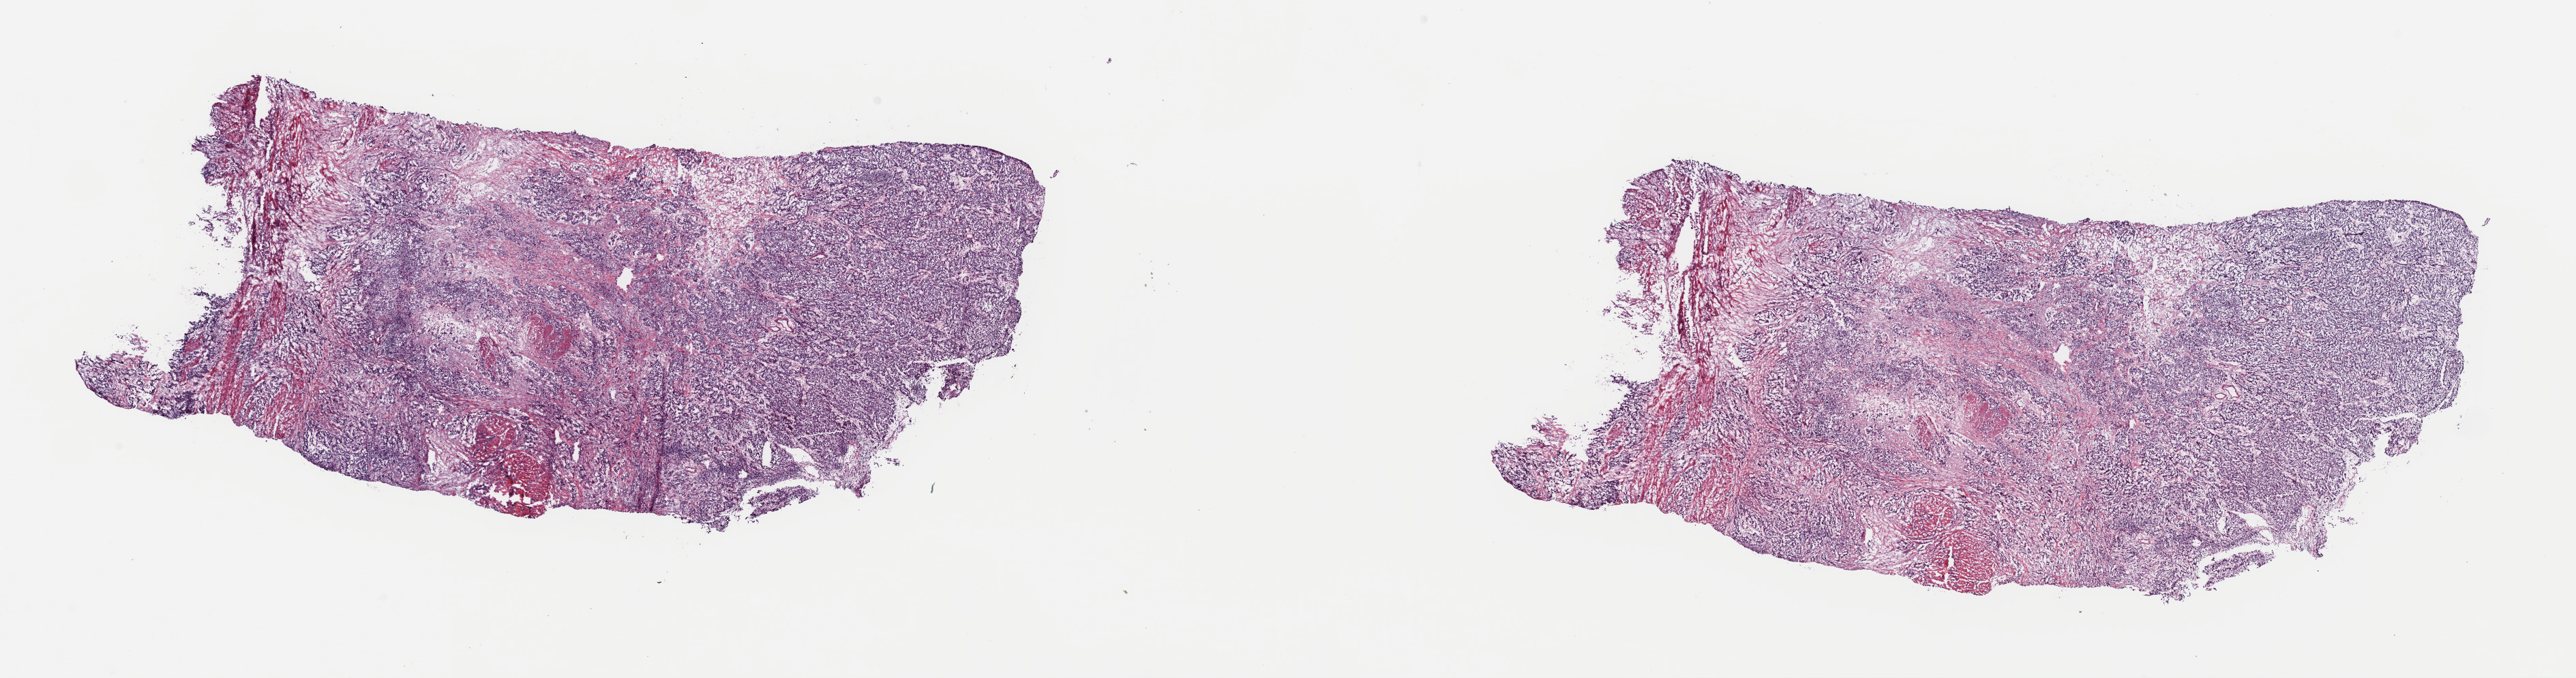
Whole-slide histology image, Hematoxylin and eosin (H&E) stained — whole scanned area (about 29.8 x 7.9 mm) shown as a low-resolution overview; frozen section; bladder, primary tumour sample. Male patient; age at initial diagnosis 58 years. Histologic grade: high grade. Pathologist review of this section (percent, as recorded): tumour cells 60%, tumour nuclei 82%, normal cells 0%, stromal cells 35%, necrosis 5%. Inflammatory infiltration, as recorded: lymphocyte infiltration 8%, monocyte infiltration 2%, neutrophil infiltration 2%.
Histologic diagnosis: Papillary transitional cell carcinoma (lateral wall of bladder). Lymph nodes positive (case pathology): 6 of 27 examined. AJCC pathologic stage: IV.